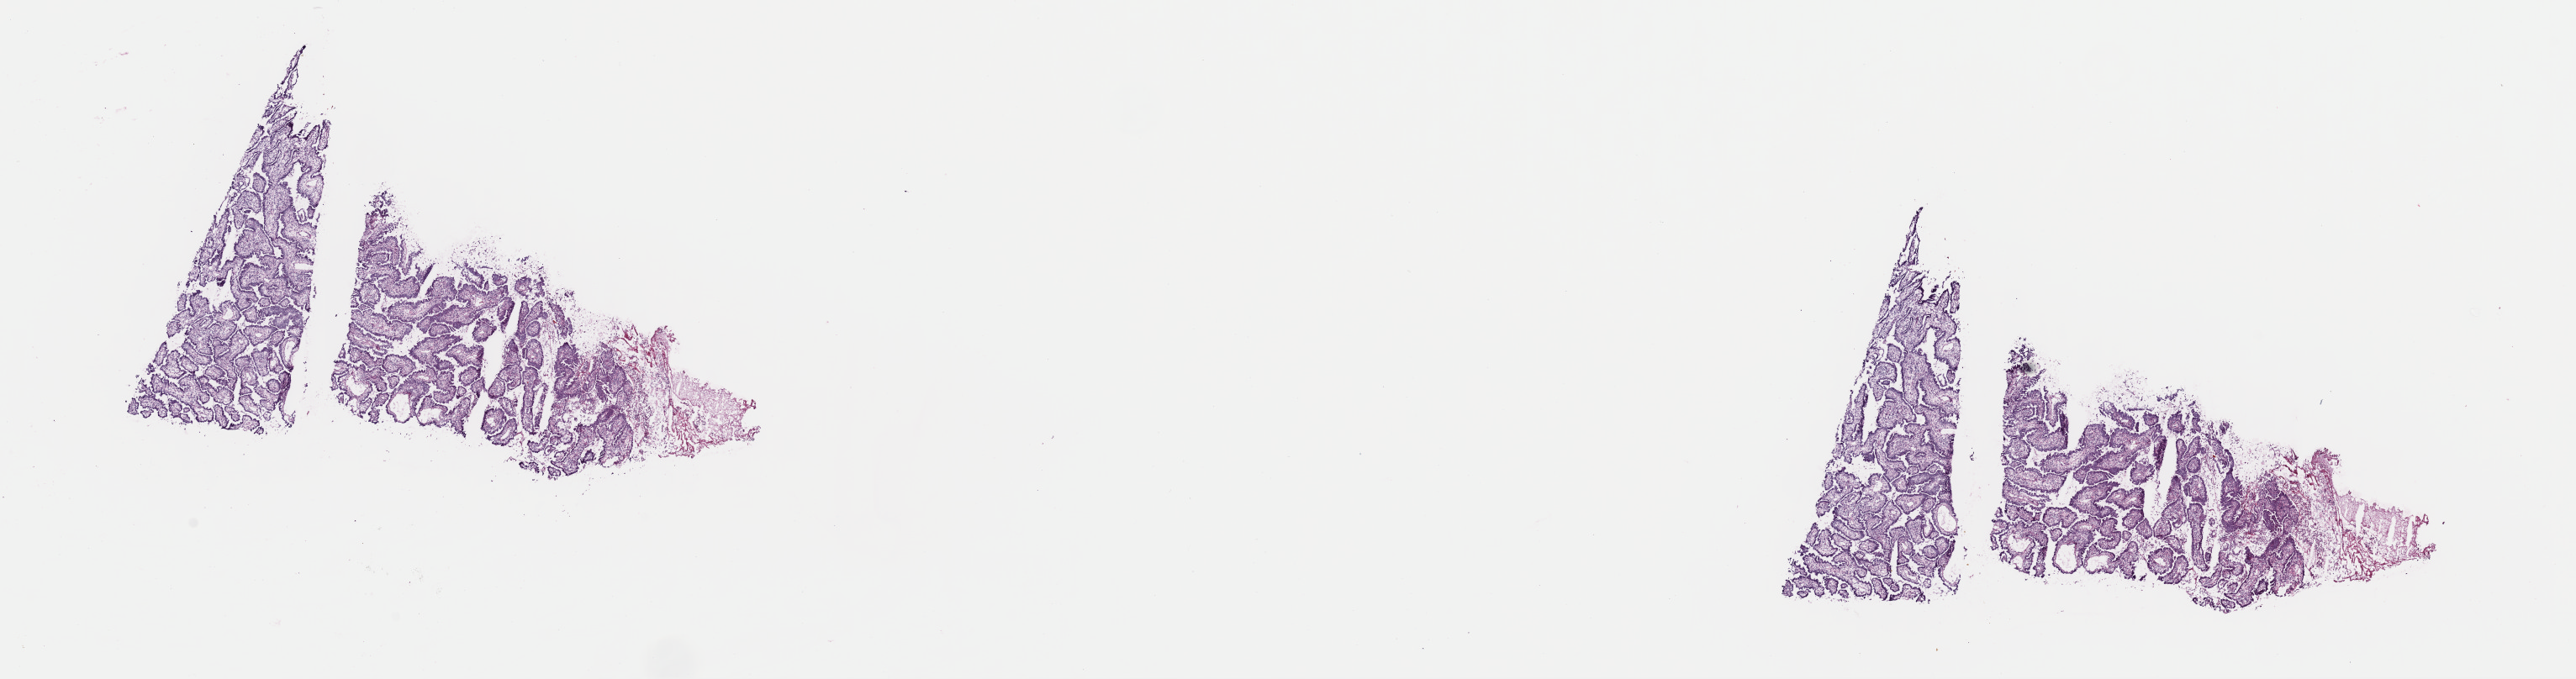
Hematoxylin and eosin (H&E) stained whole-slide image — whole scanned area (about 24.2 x 6.4 mm) shown as a low-resolution overview, frozen section from the top of the tissue portion, sample: primary tumour, cervix. Patient: female, age at initial diagnosis 33 years.
Pathologic diagnosis: Adenocarcinoma, endocervical type.